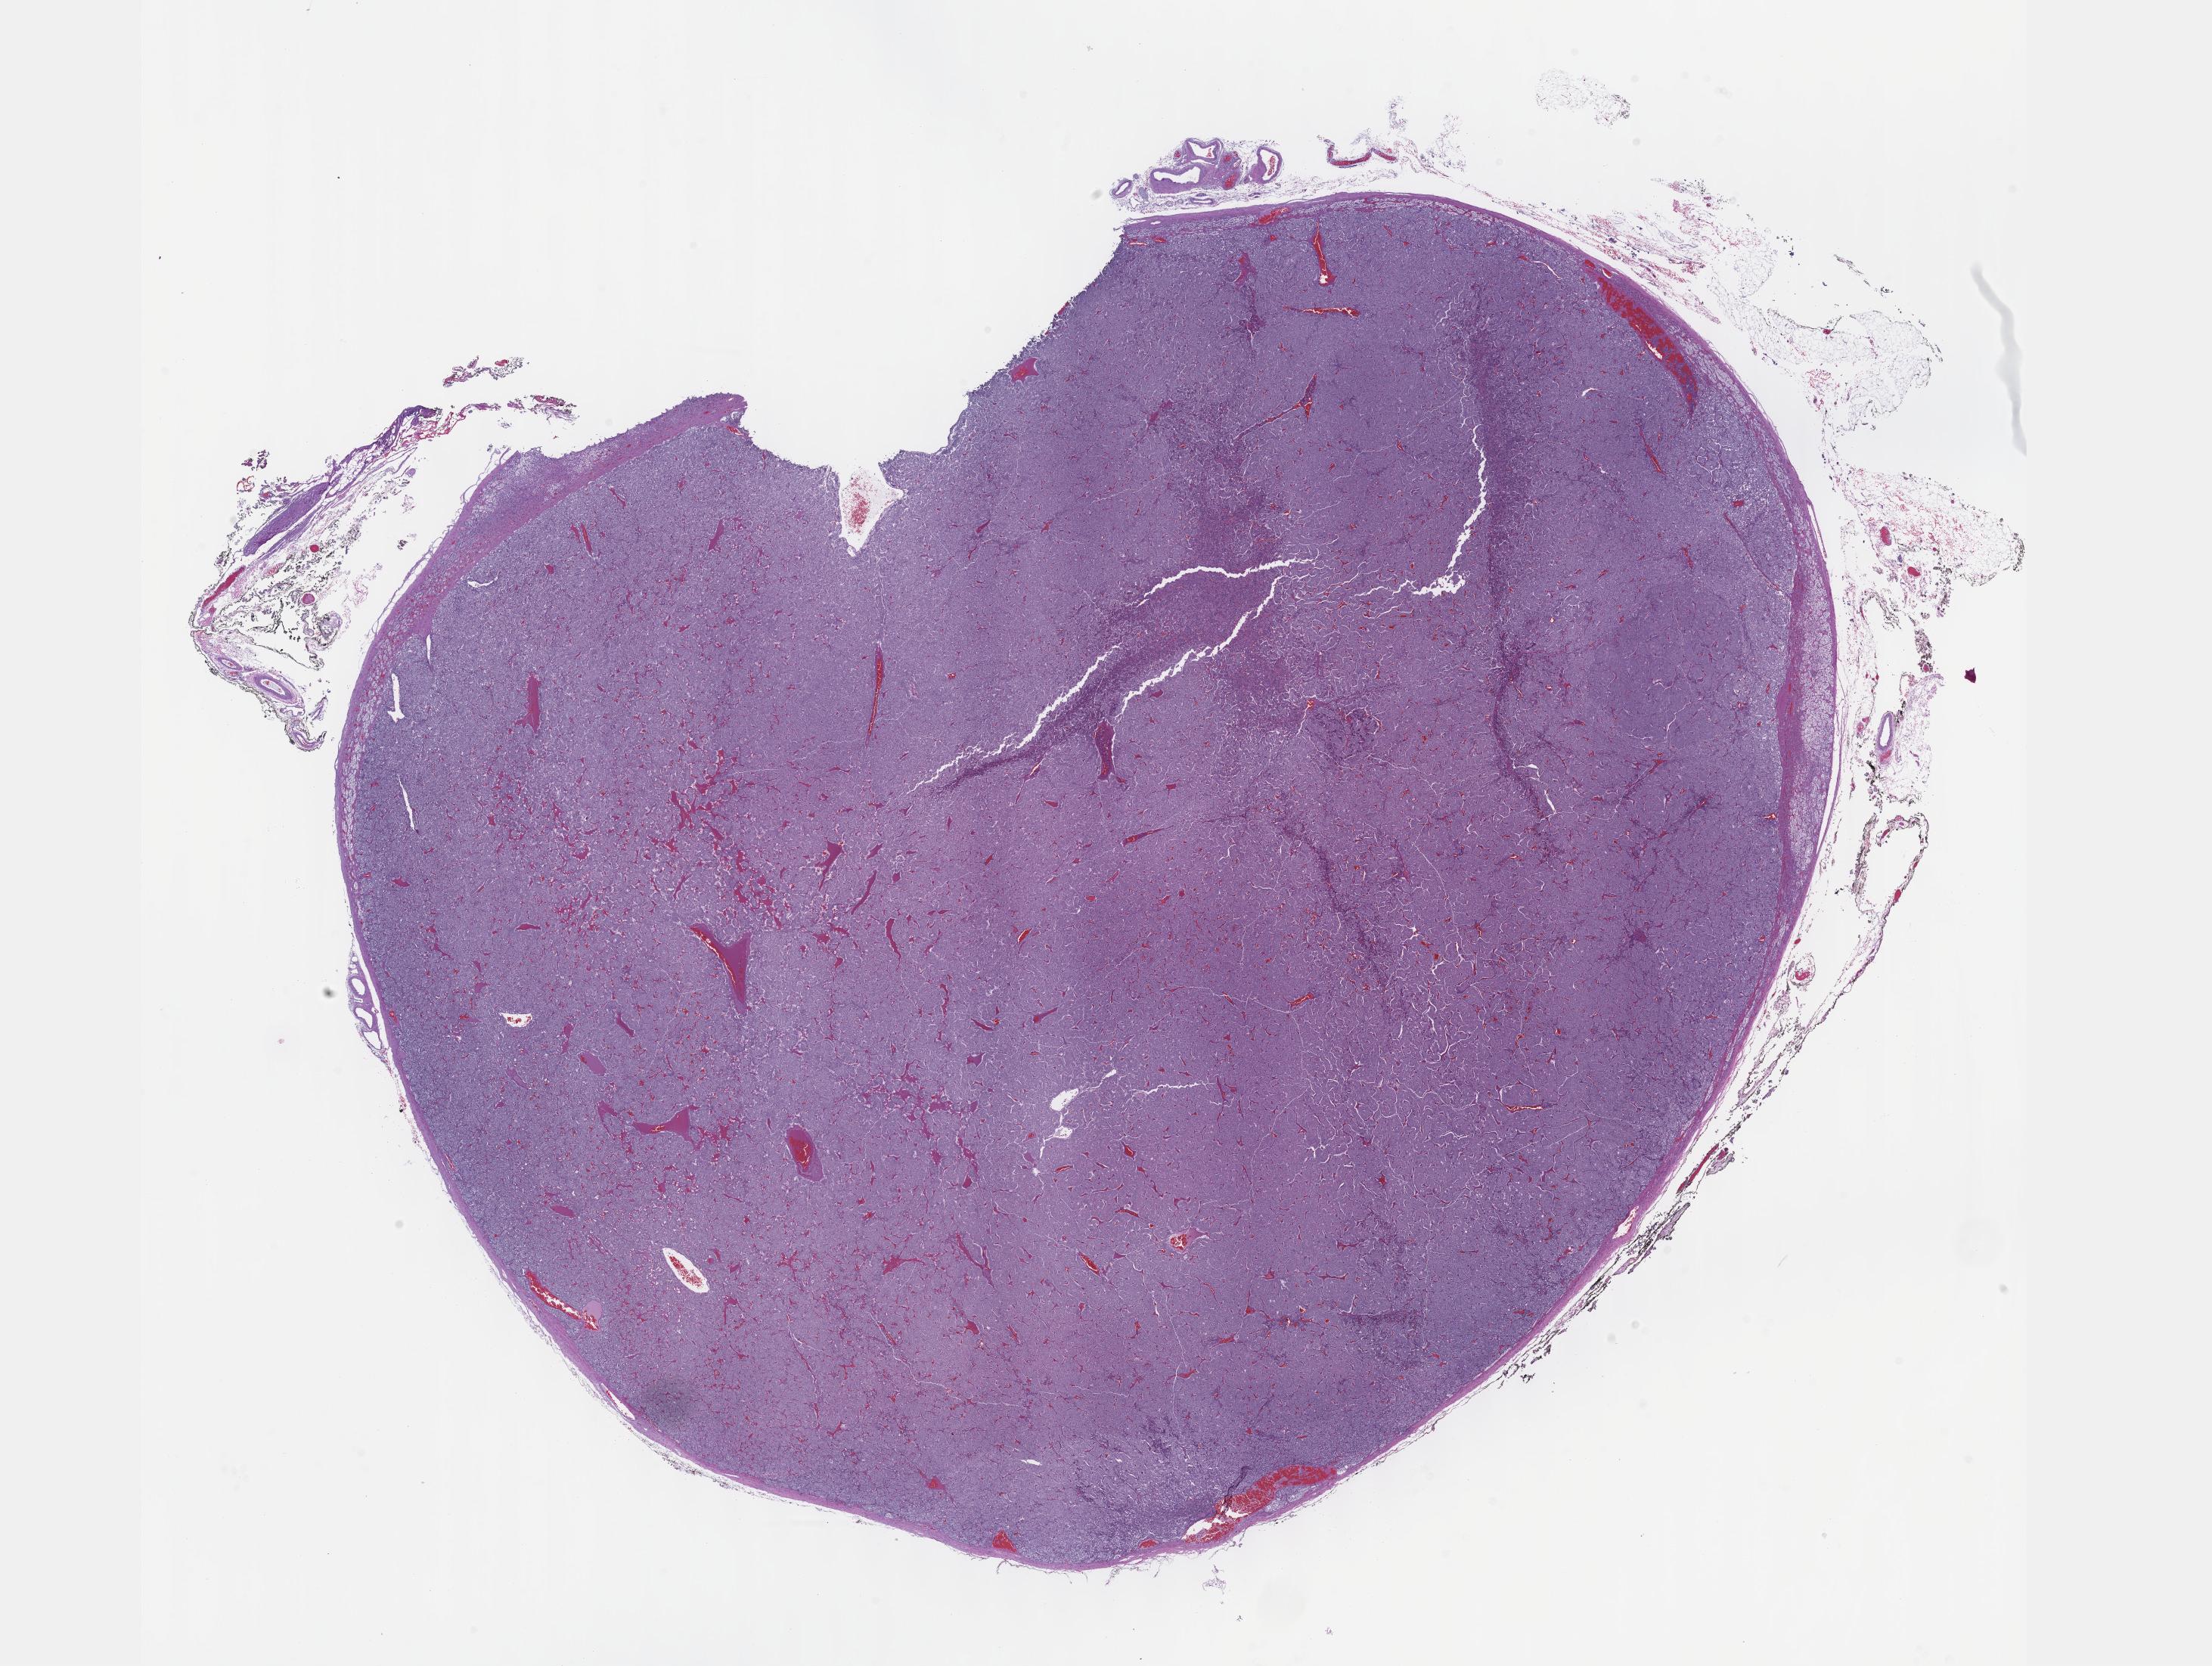
Hematoxylin and eosin (H&E) stained whole-slide image, low-resolution overview of the scanned area, about 23.6 x 17.8 mm. FFPE section. Sample: primary tumour, adrenal gland. Female patient; age at initial diagnosis 31 years.
• diagnosis: Pheochromocytoma, NOS